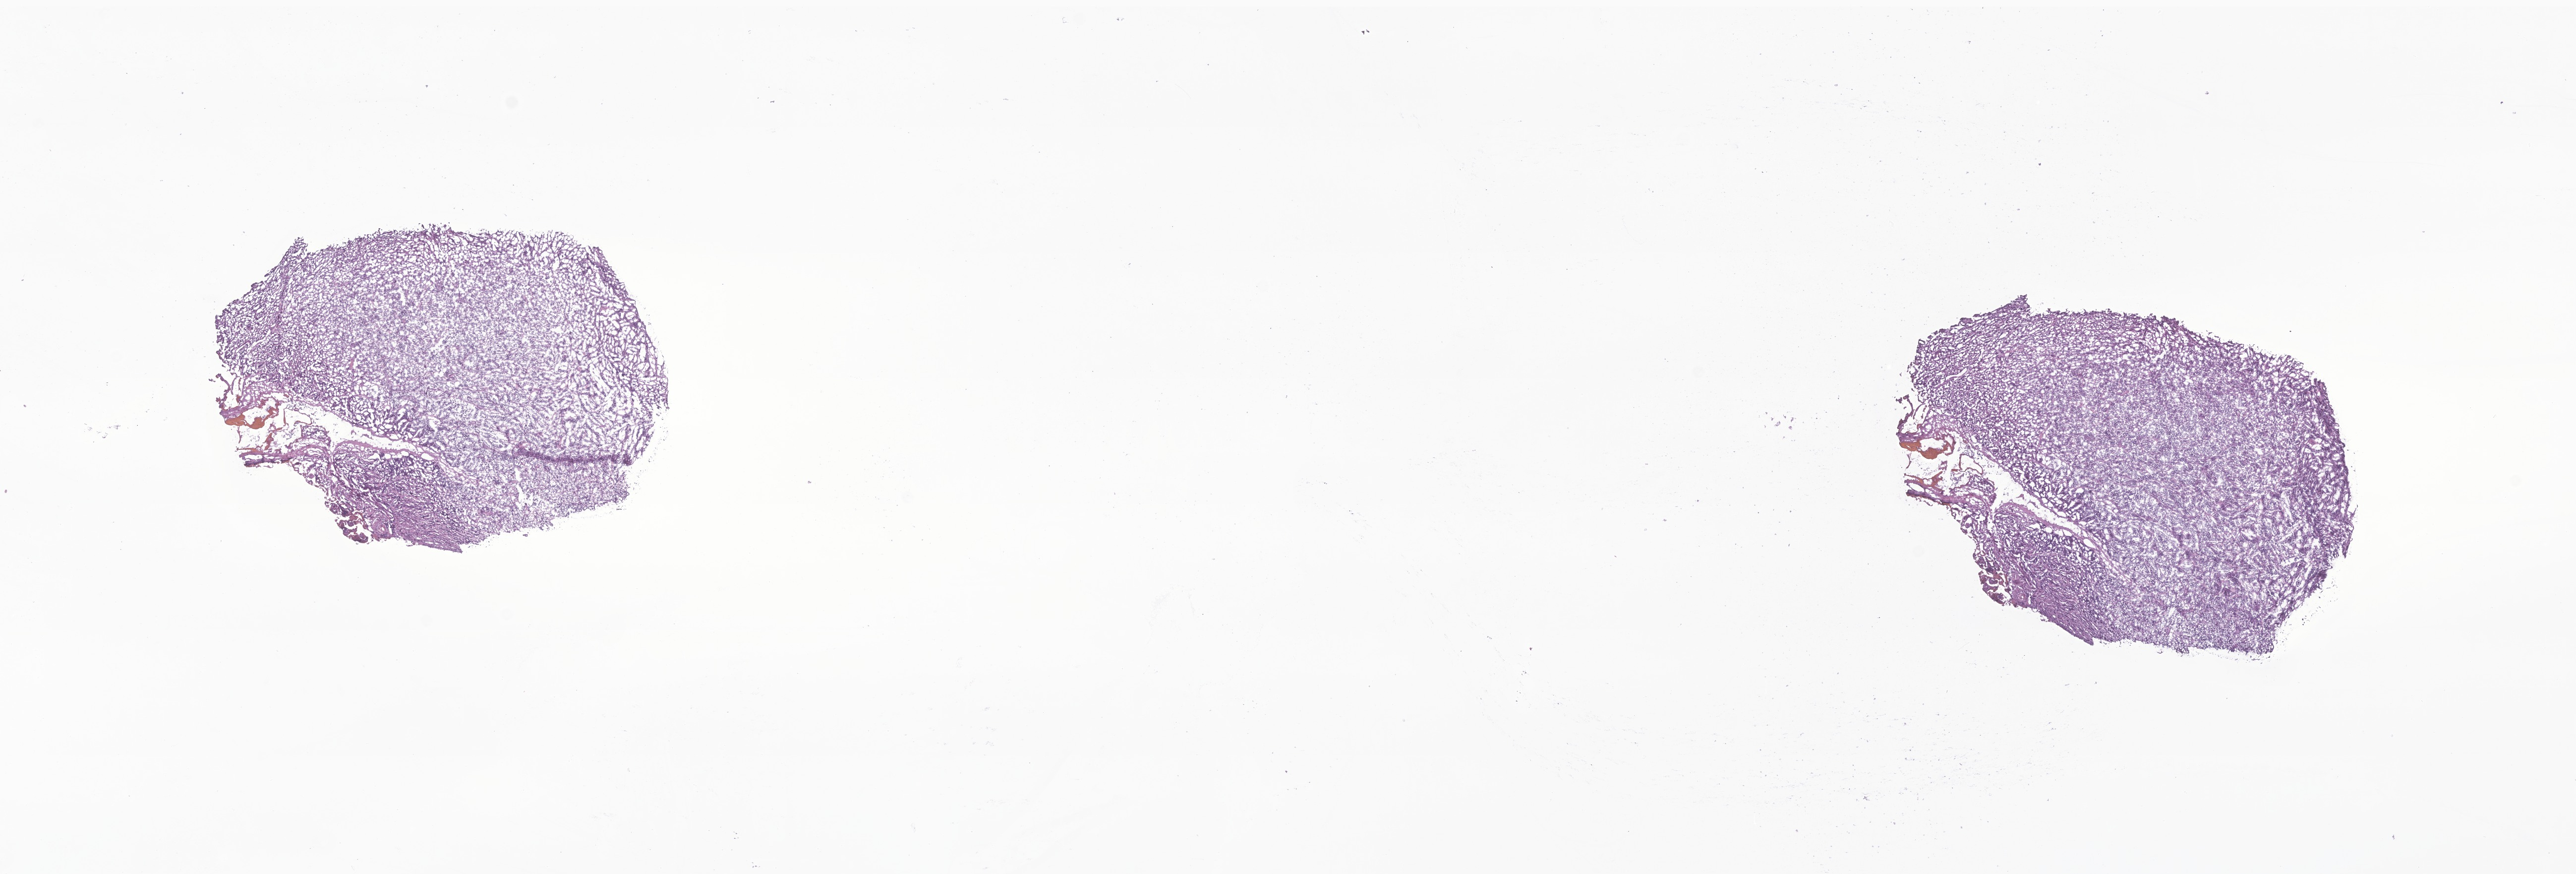
Digitized hematoxylin and eosin (H&E)-stained section of tumor tissue from the brain, low-resolution overview of the scanned area, about 21.9 x 7.4 mm, frozen section (OCT-embedded). Male patient, age 40 months (3 years 4 months).
Diagnosis: Medulloblastoma, NOS.